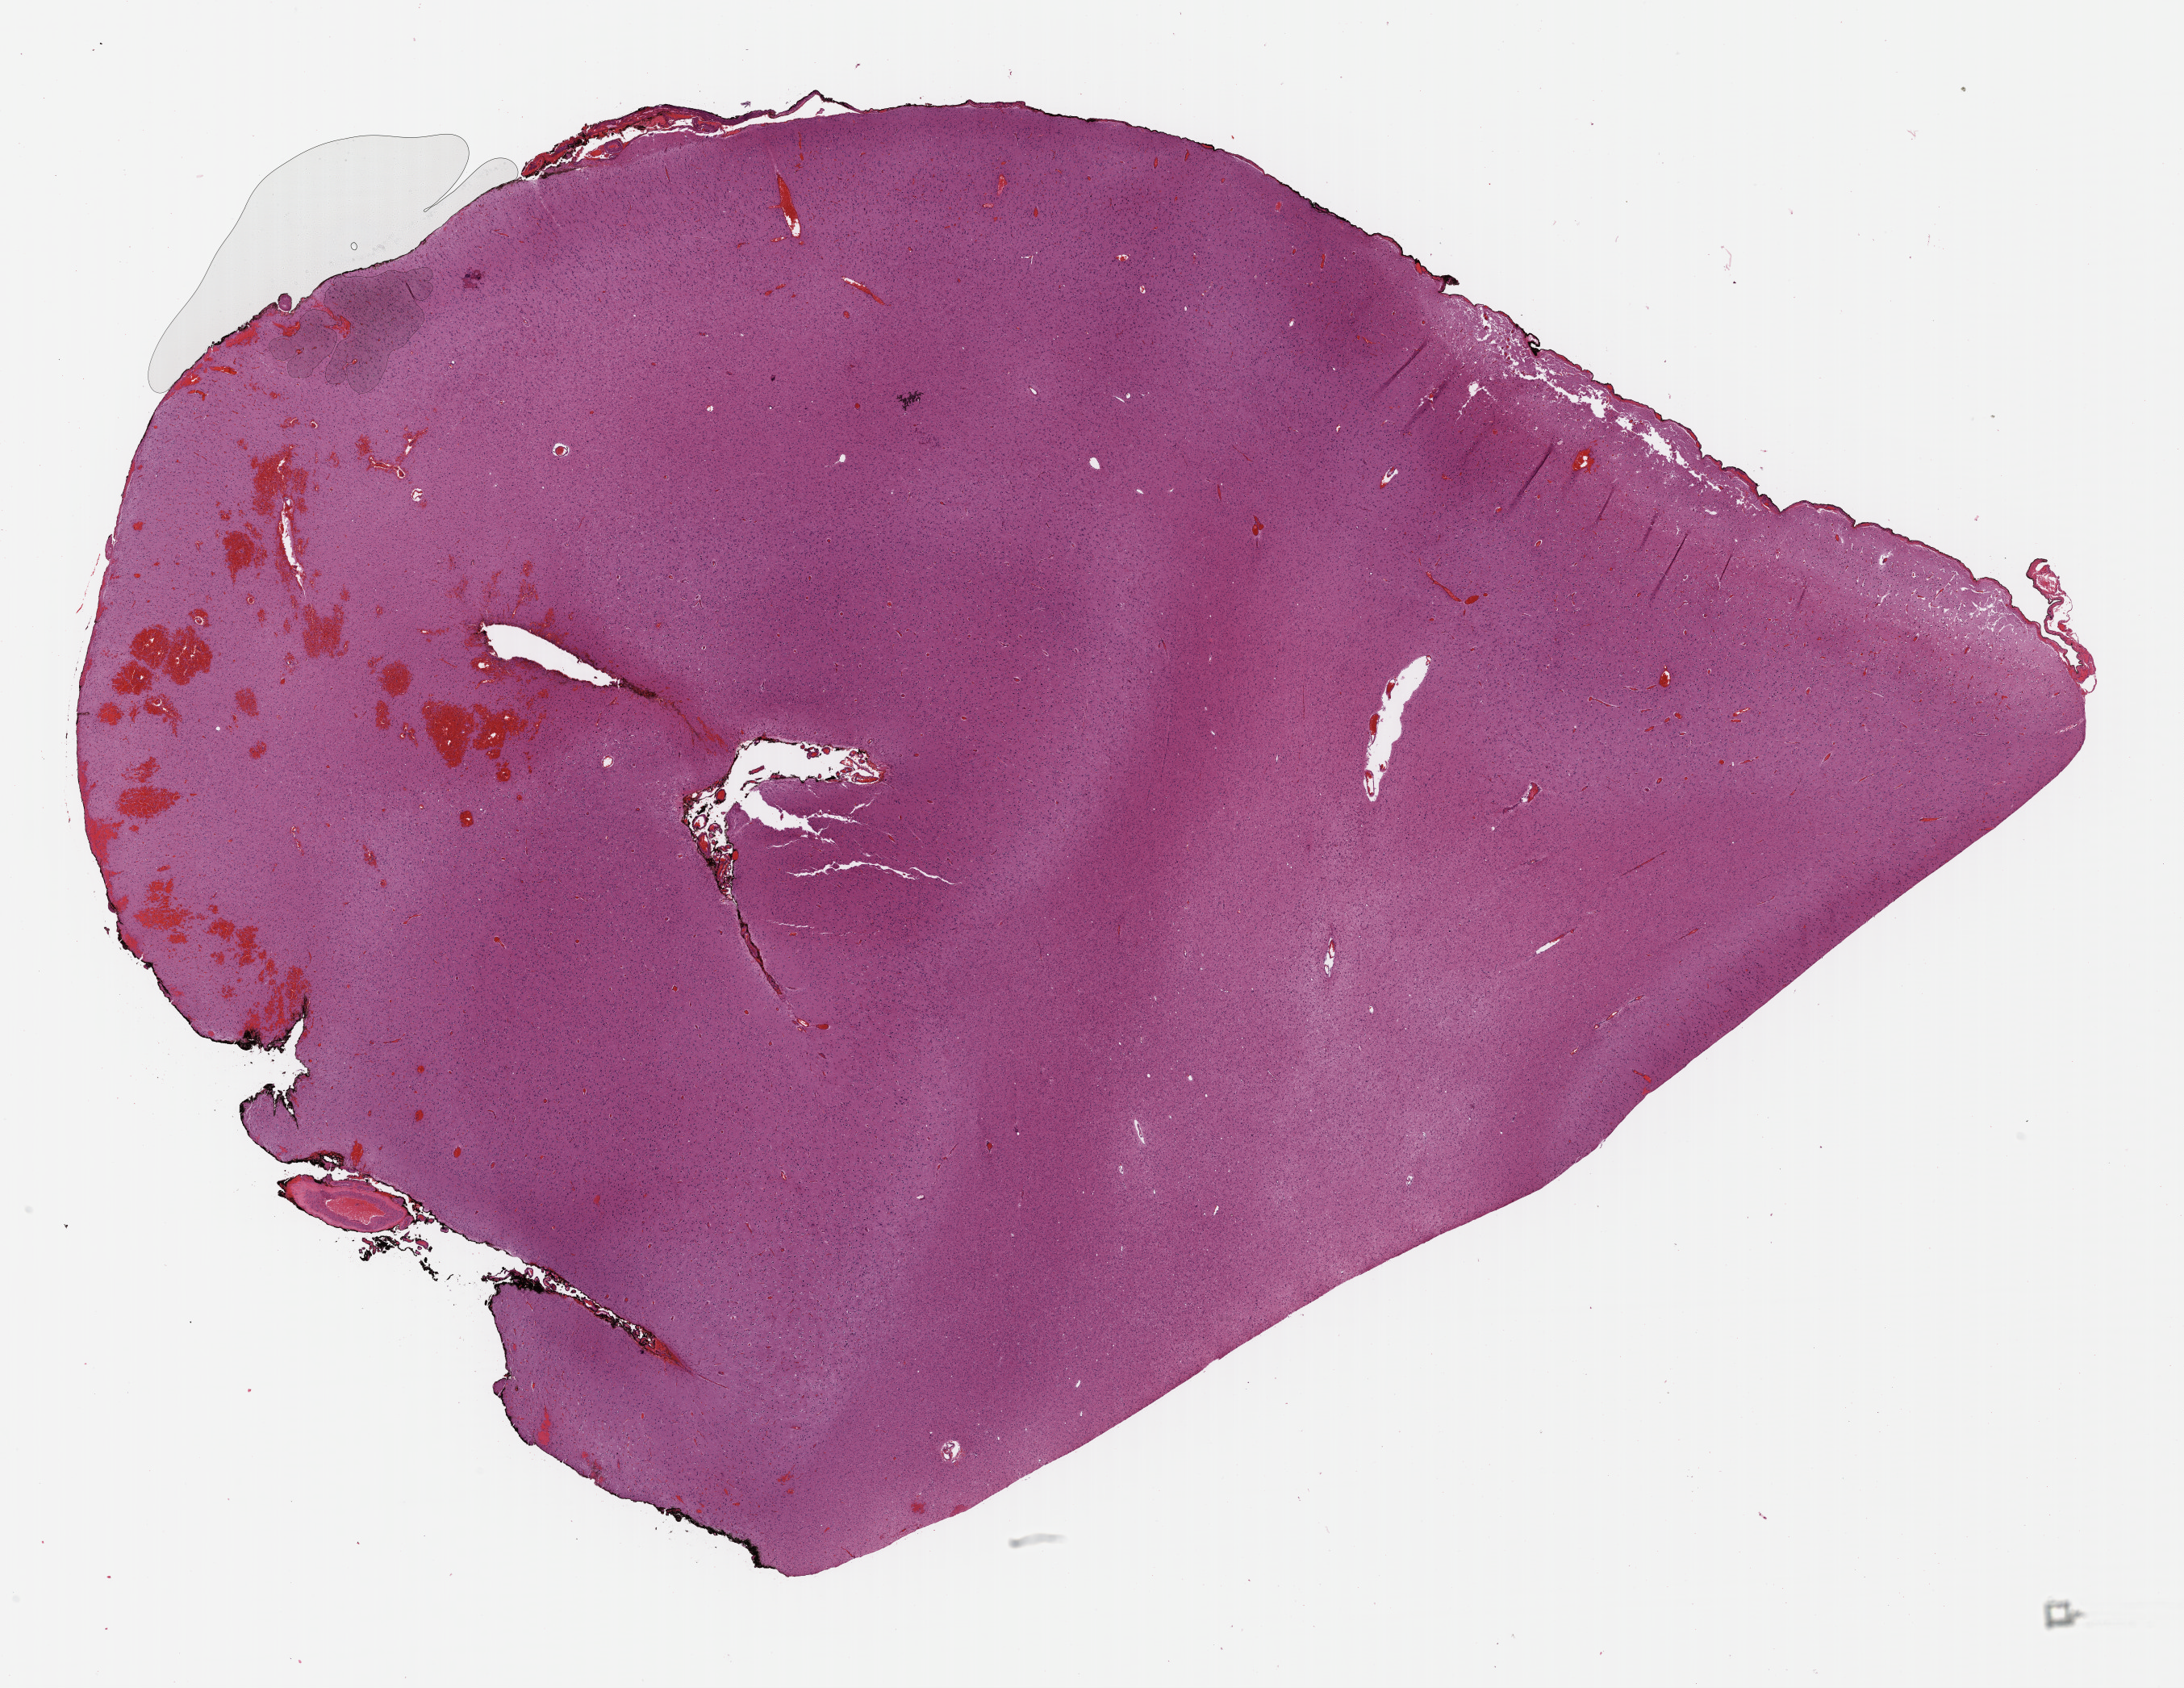
Whole-slide histology image, Hematoxylin and eosin (H&E) stained, a low-resolution overview of the entire scanned area, about 21.3 x 16.4 mm; FFPE section; primary tumour sample from the brain. Female patient; age at initial diagnosis 61 years. Histologic grade: G2 (moderately differentiated).
Laterality: left. Pathologic diagnosis: Astrocytoma, NOS (cerebrum).